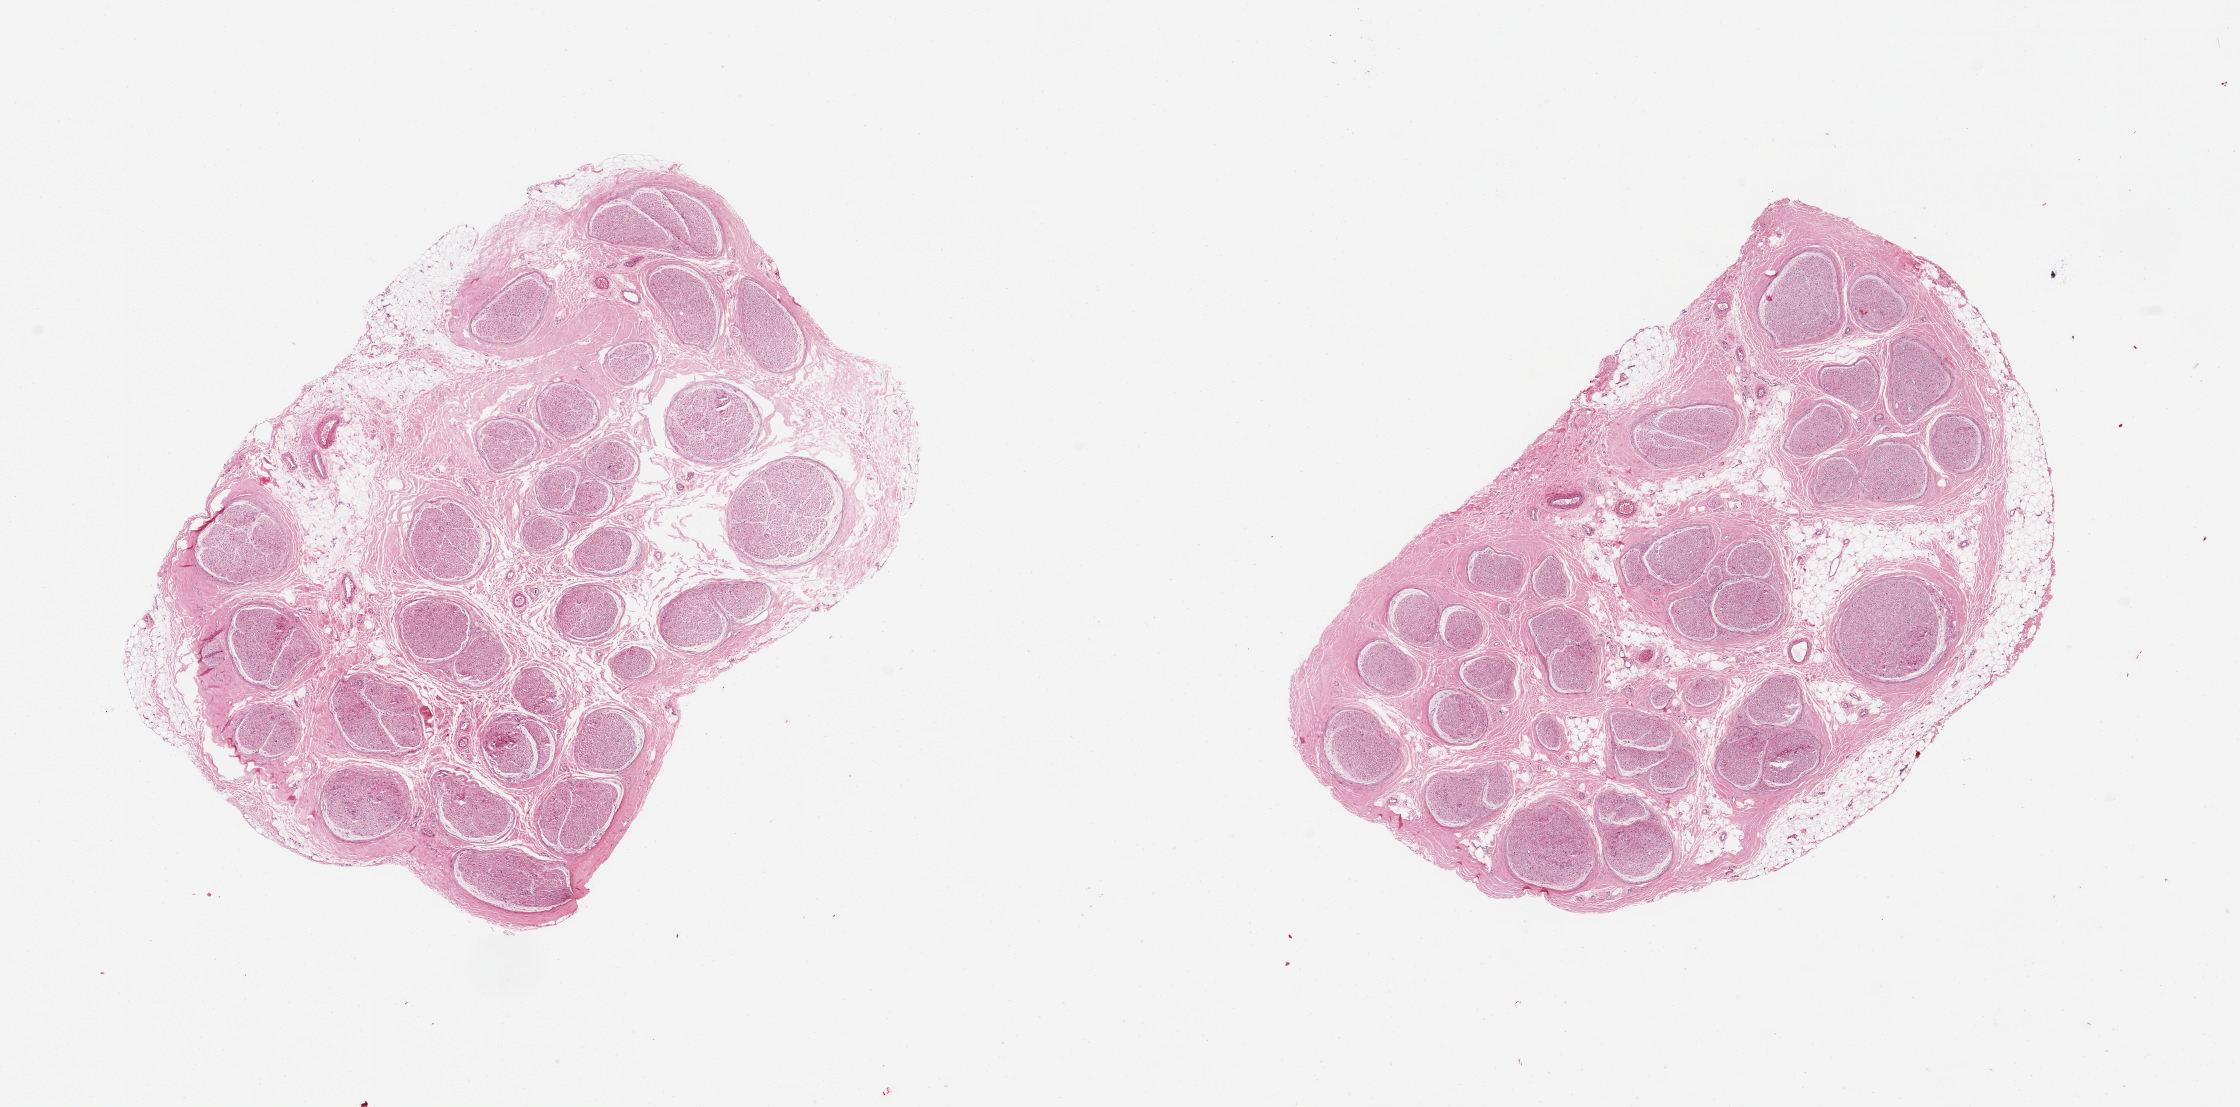
Whole-slide image, H&E stain, shown as a low-resolution overview of the whole scanned area (about 17.7 x 8.8 mm, acquisition: 20x scan), PAXgene-fixed paraffin-embedded (PFPE) section, section of tibial nerve (target tissue), tissue donor sample.
Pathologist's review note for this sample: 2 pieces, trace partial rim of adherent fat up to ~0.3mm.